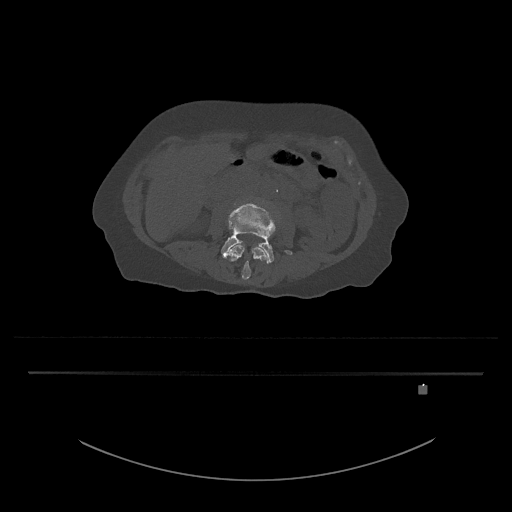
CT including the spine, one axial slice; slice 392 of 797 in the series (ordered by position); 120 kVp; bone window (W 1800 / L 400 HU); 0.5 mm slice thickness; 512 × 512 image matrix, field of view 500 × 500 mm. Female patient, age 57 years. From the clinical record (not read from this slice): primary cancer: cervical.
Annotated regions visible in this slice (semi-automatic segmentation, software-assisted and operator-edited):
- L3 vertebra: box from (x=227, y=243) to (x=268, y=280) px
- L4 vertebra: (x=221, y=203)–(x=292, y=264)